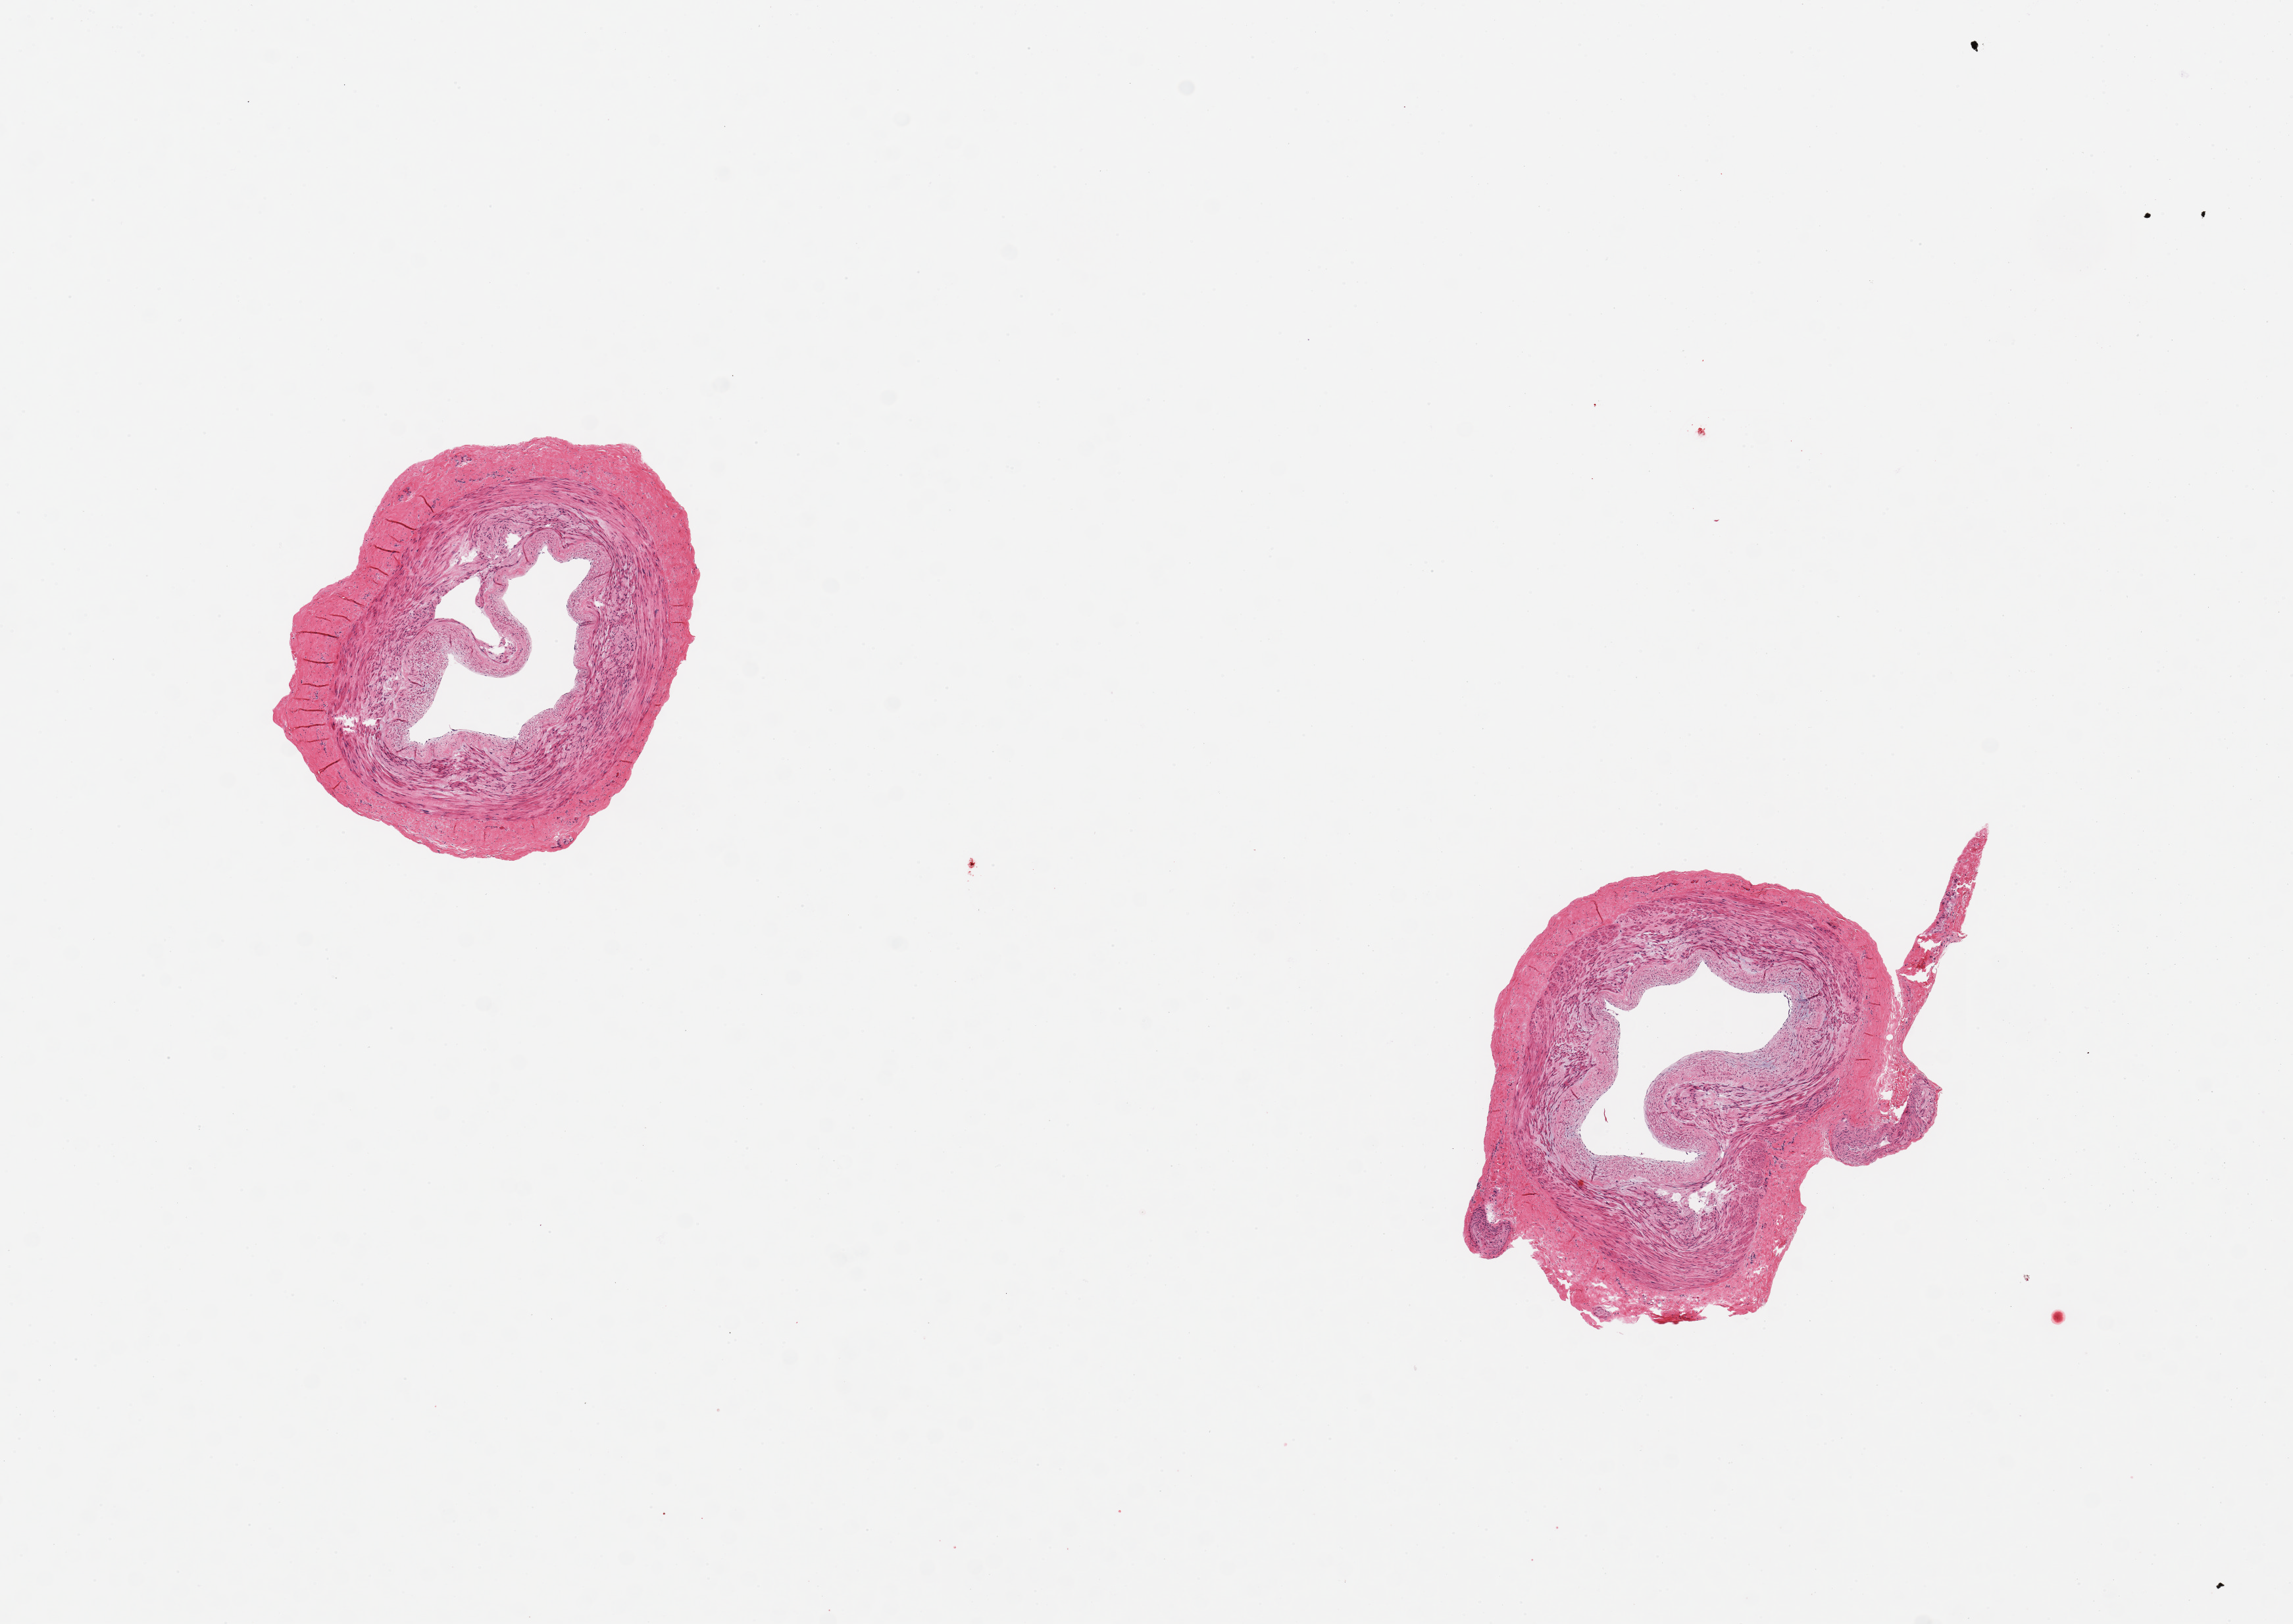
Haematoxylin and eosin whole-slide image, brightfield — shown as a low-resolution overview of the whole scanned area (about 13.8 x 9.8 mm). PAXgene-fixed paraffin-embedded (PFPE) section. Section of tibial artery (target tissue). Tissue donor sample. Donor: male.
Review note (as recorded): 2 pieces, 2.7 & 3mm in diameter; no extraneous adipose.